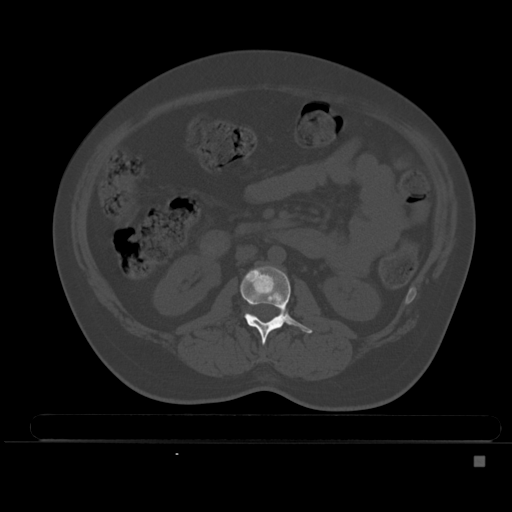
CT including the spine, one axial slice; position 171 of 495 along the scan axis; bone window (W 1800 / L 400 HU); 1.5 mm slice thickness; 512 × 512 image matrix, field of view 404 × 404 mm. Female patient, age 33 years. From the clinical record (not read from this slice): primary cancer: breast.
Structures marked on this image (semi-automatically segmented with operator editing):
- L2 vertebra: box from (x=240, y=266) to (x=313, y=345) px